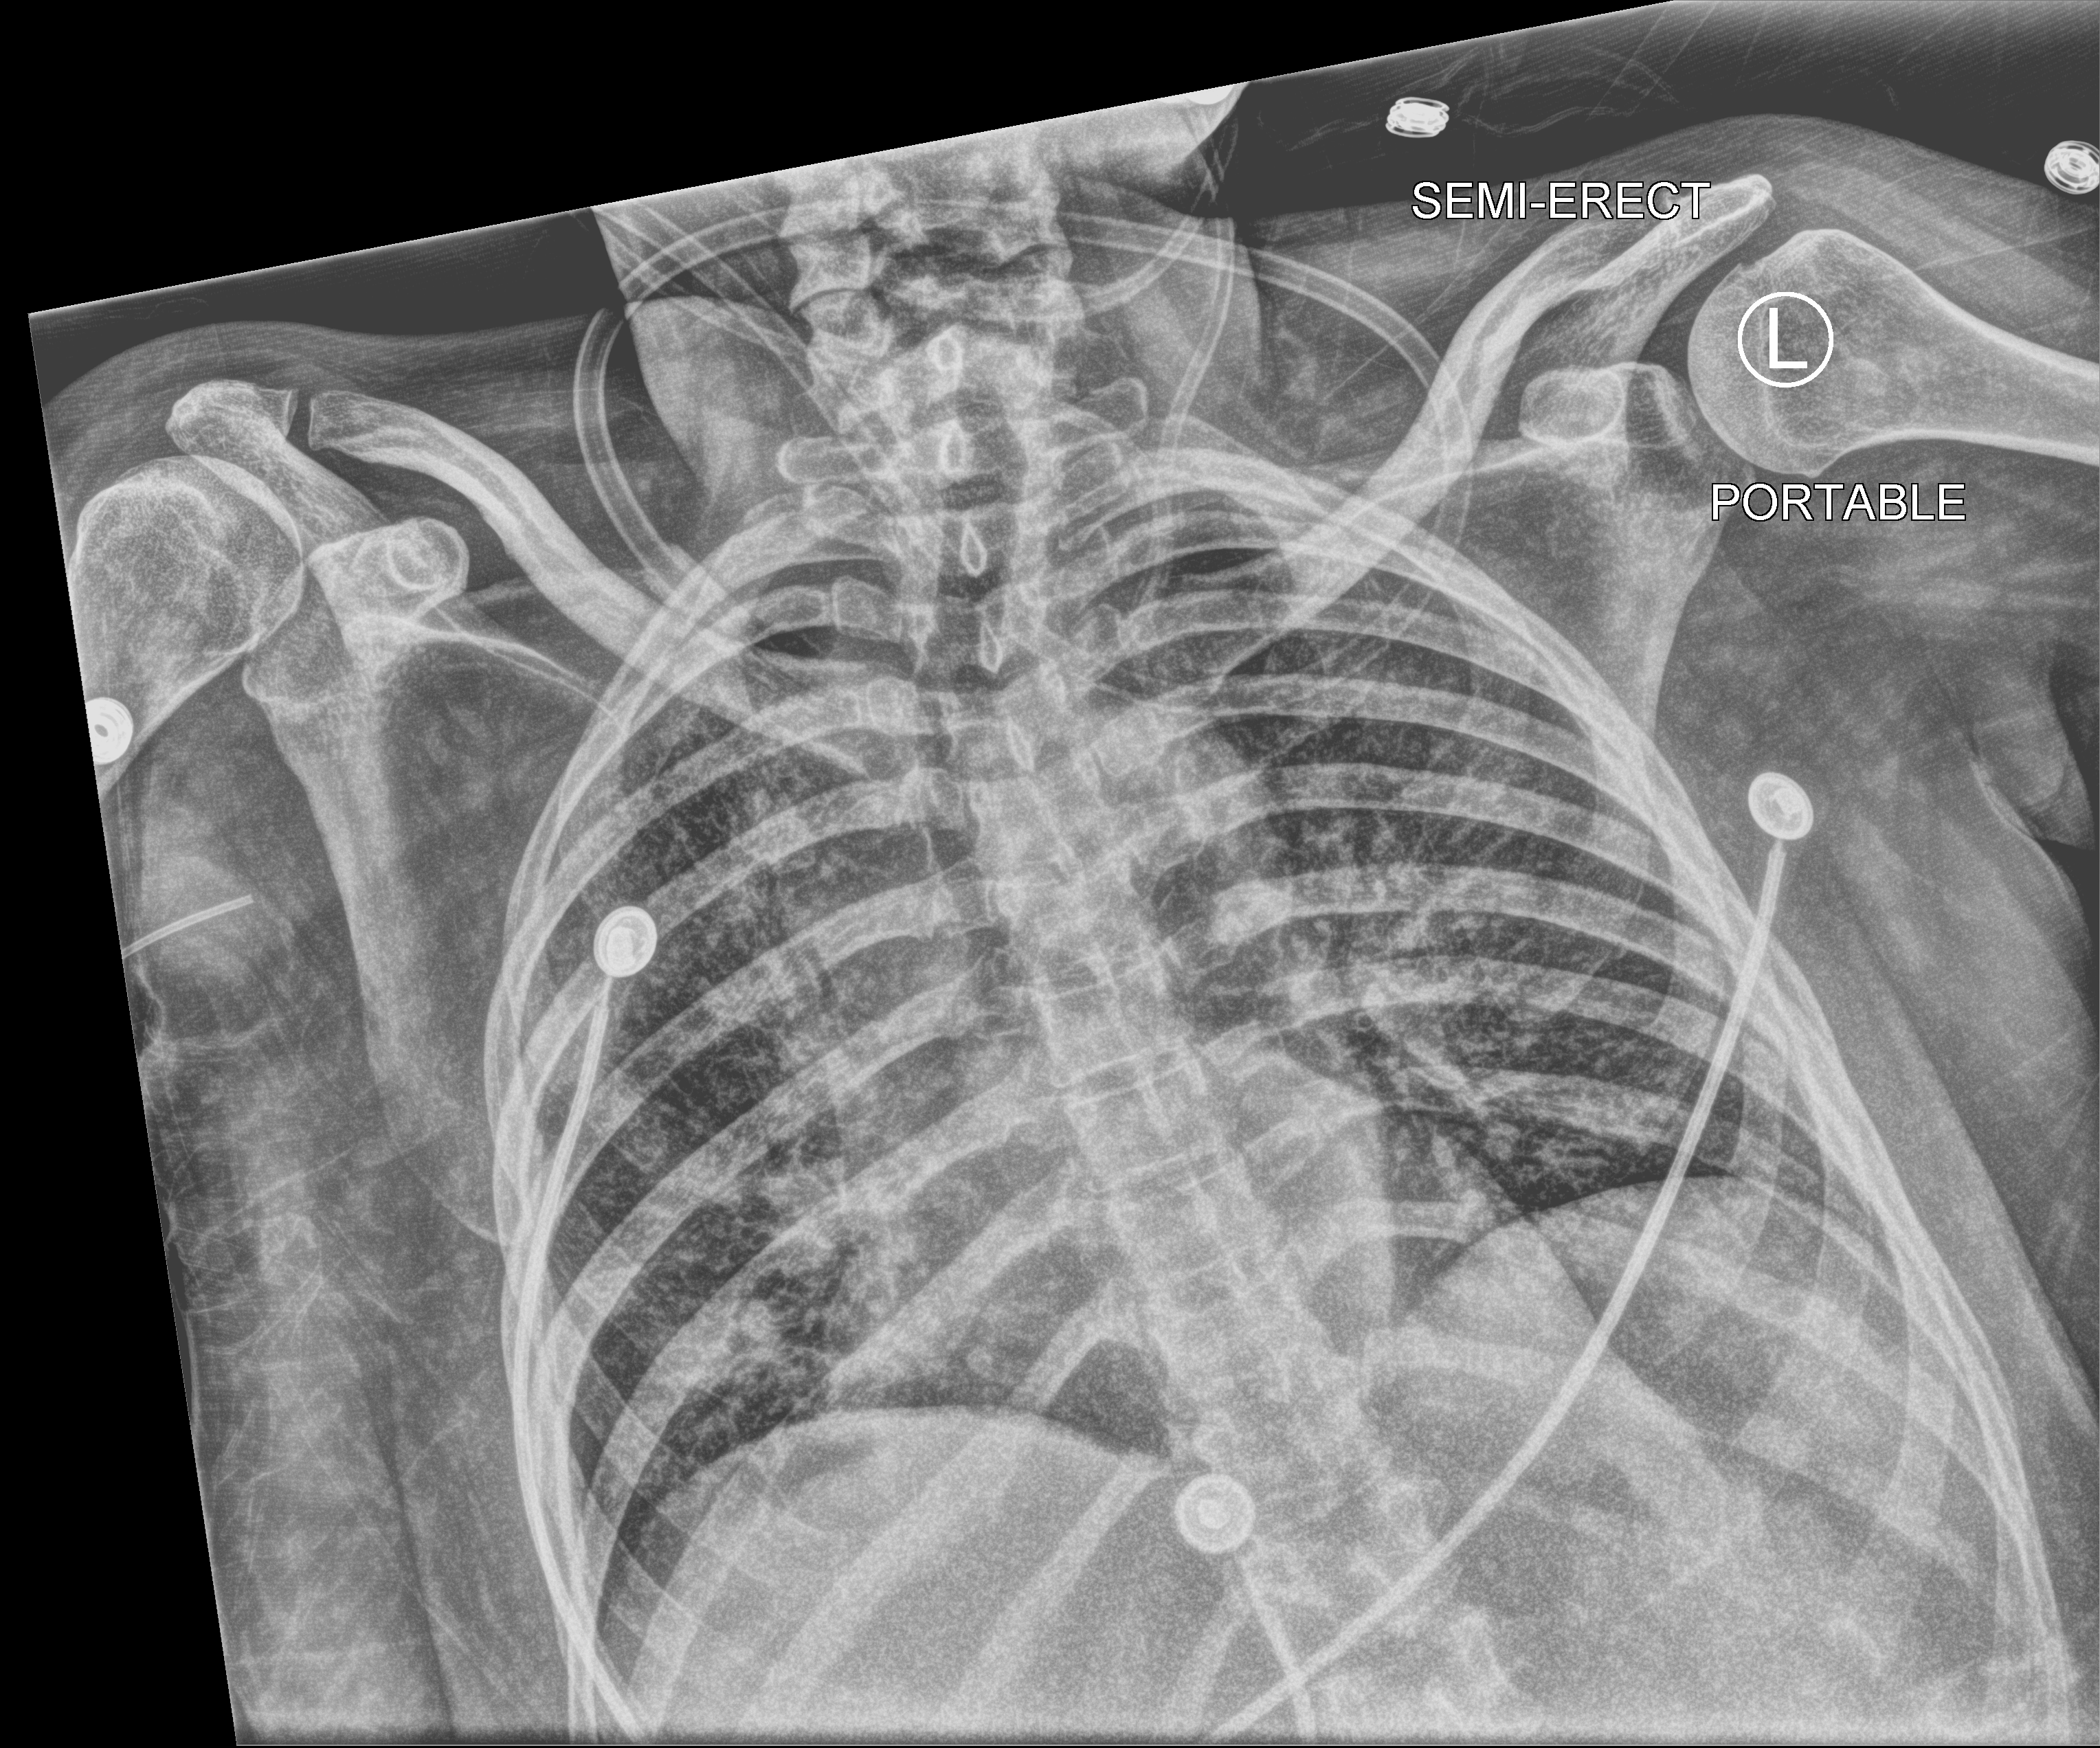
Chest X-ray (portable); anteroposterior (AP) projection. Female patient hospitalised with COVID-19, age 18–59 years.
Hospital-stay facts (about this admission, not read from this image; timing relative to this image not recorded): mechanically ventilated during this hospital stay: no; admitted to intensive care during this hospital stay: no; hypertension (admission record): yes.